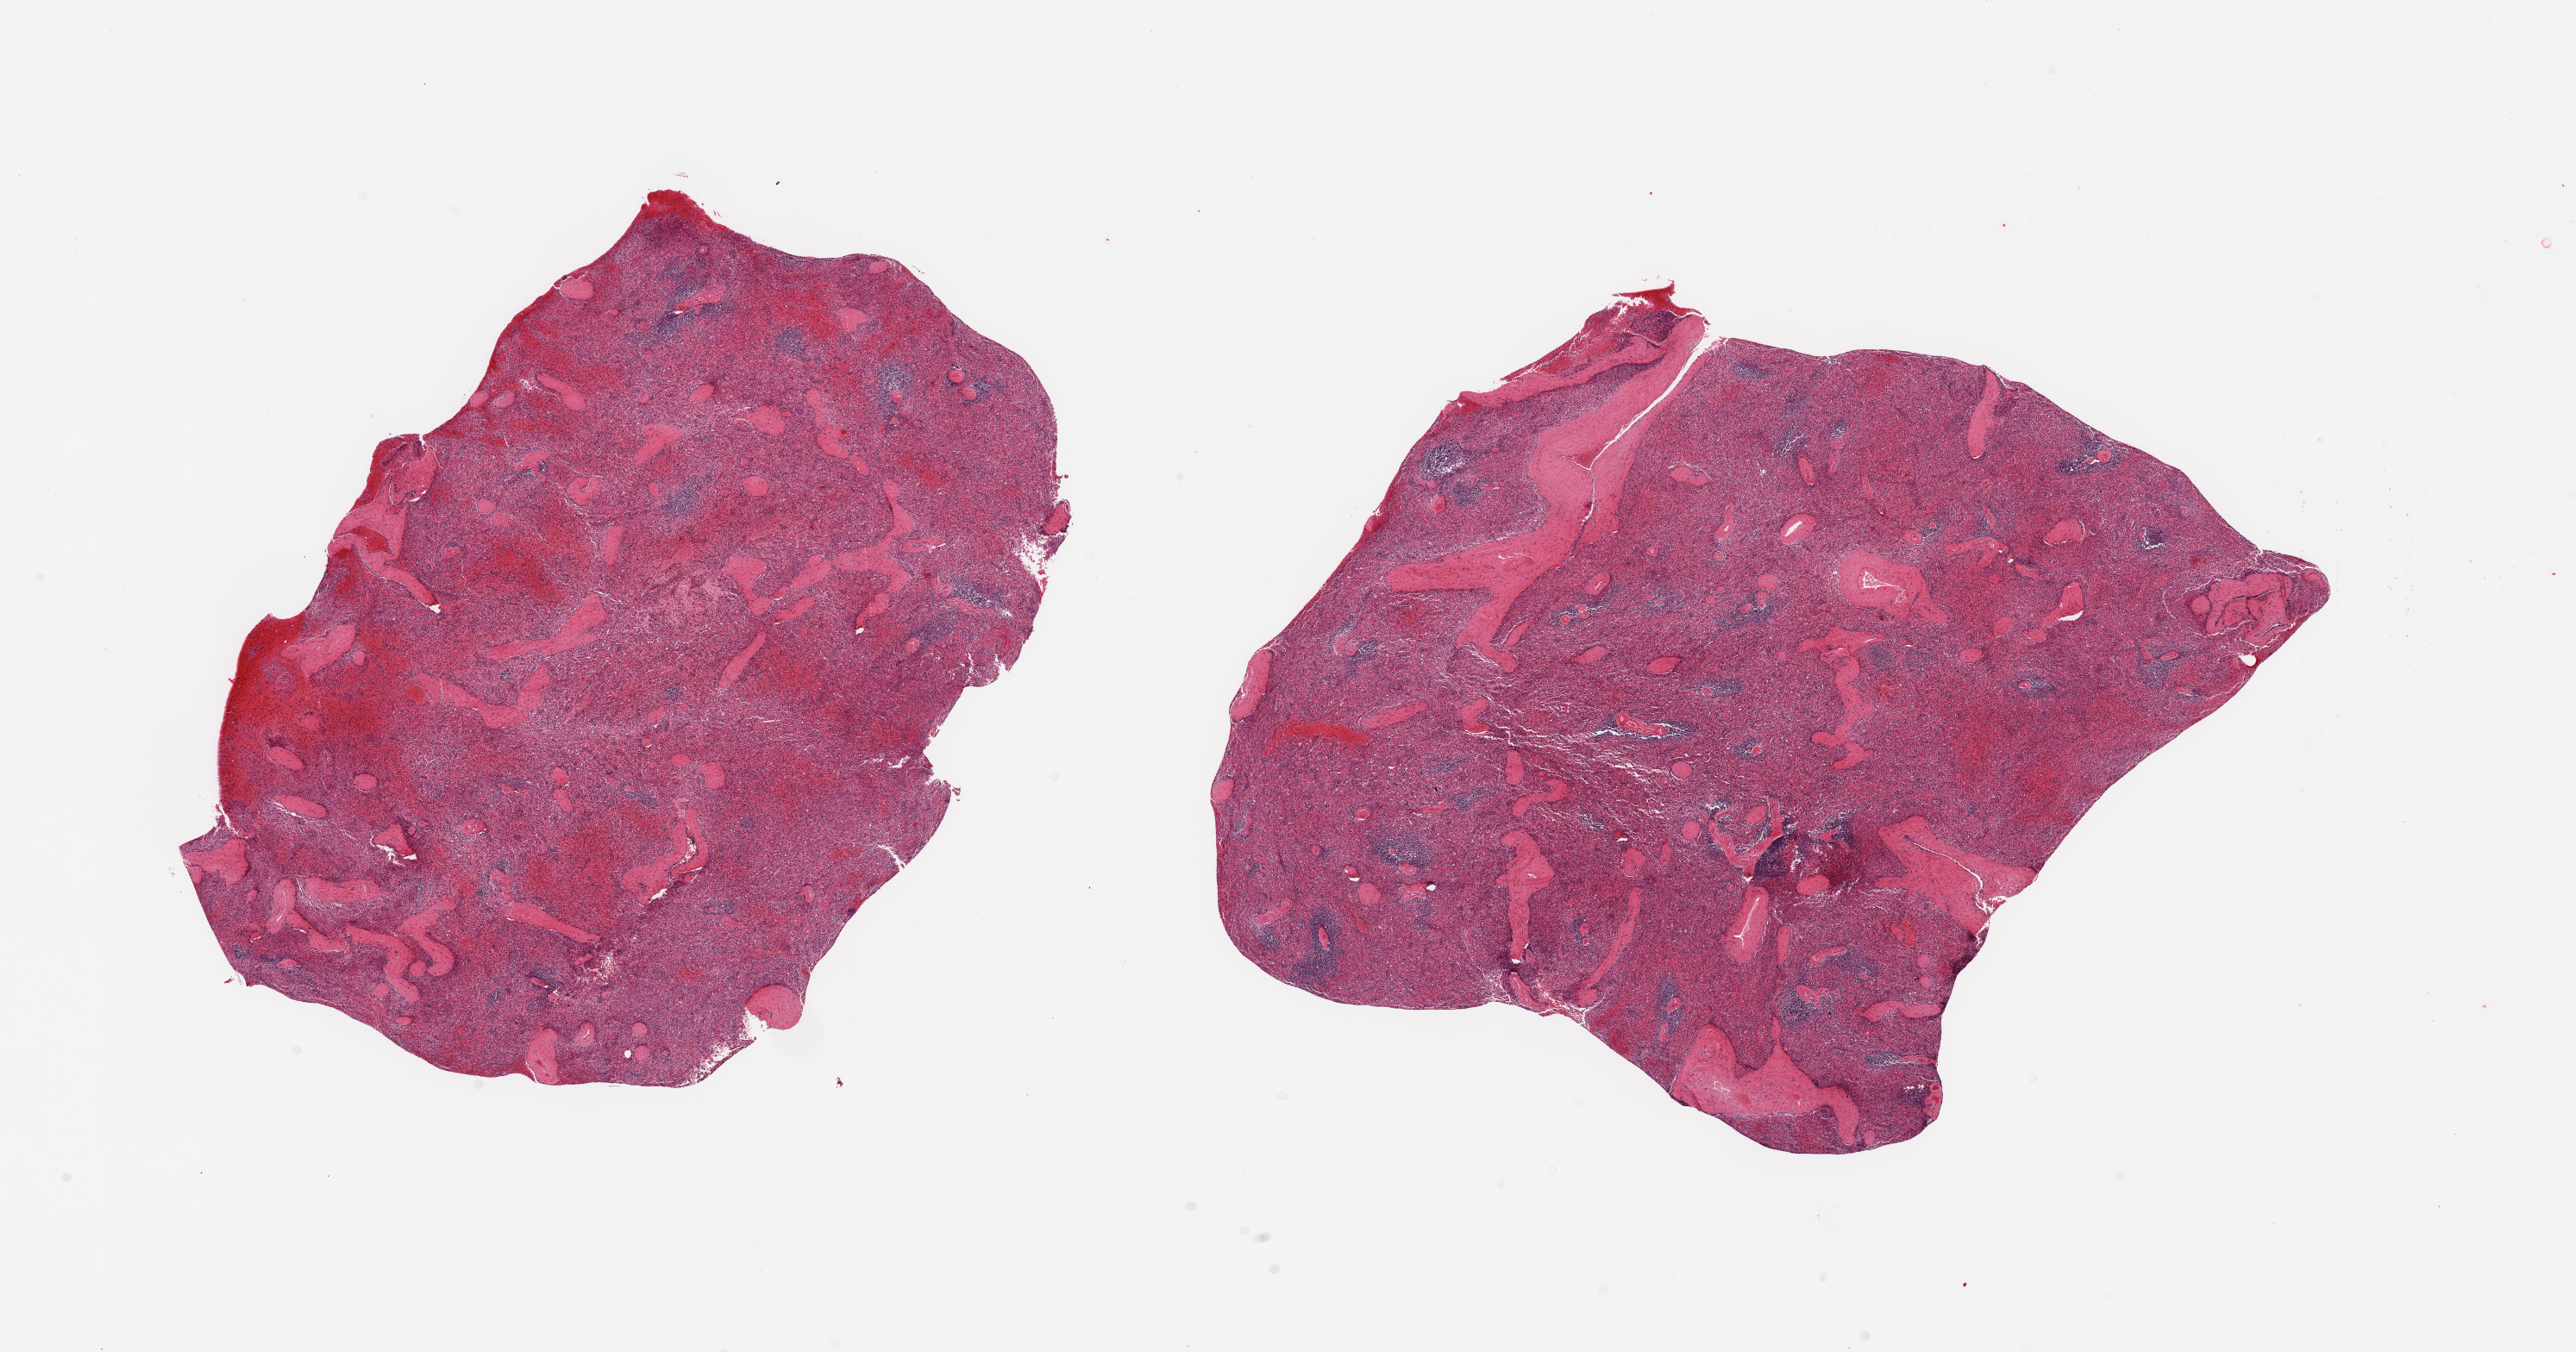
Whole-slide image, H&E stain, a low-resolution overview of the entire scanned area, about 23.6 x 12.4 mm, PAXgene-fixed paraffin-embedded (PFPE) section, section of spleen (target tissue), tissue donor sample. Donor sex: female.
Reviewer comment on this tissue sample: 2 pieces; mild congestion; prominent fibrous trabeculae occupy 10%.